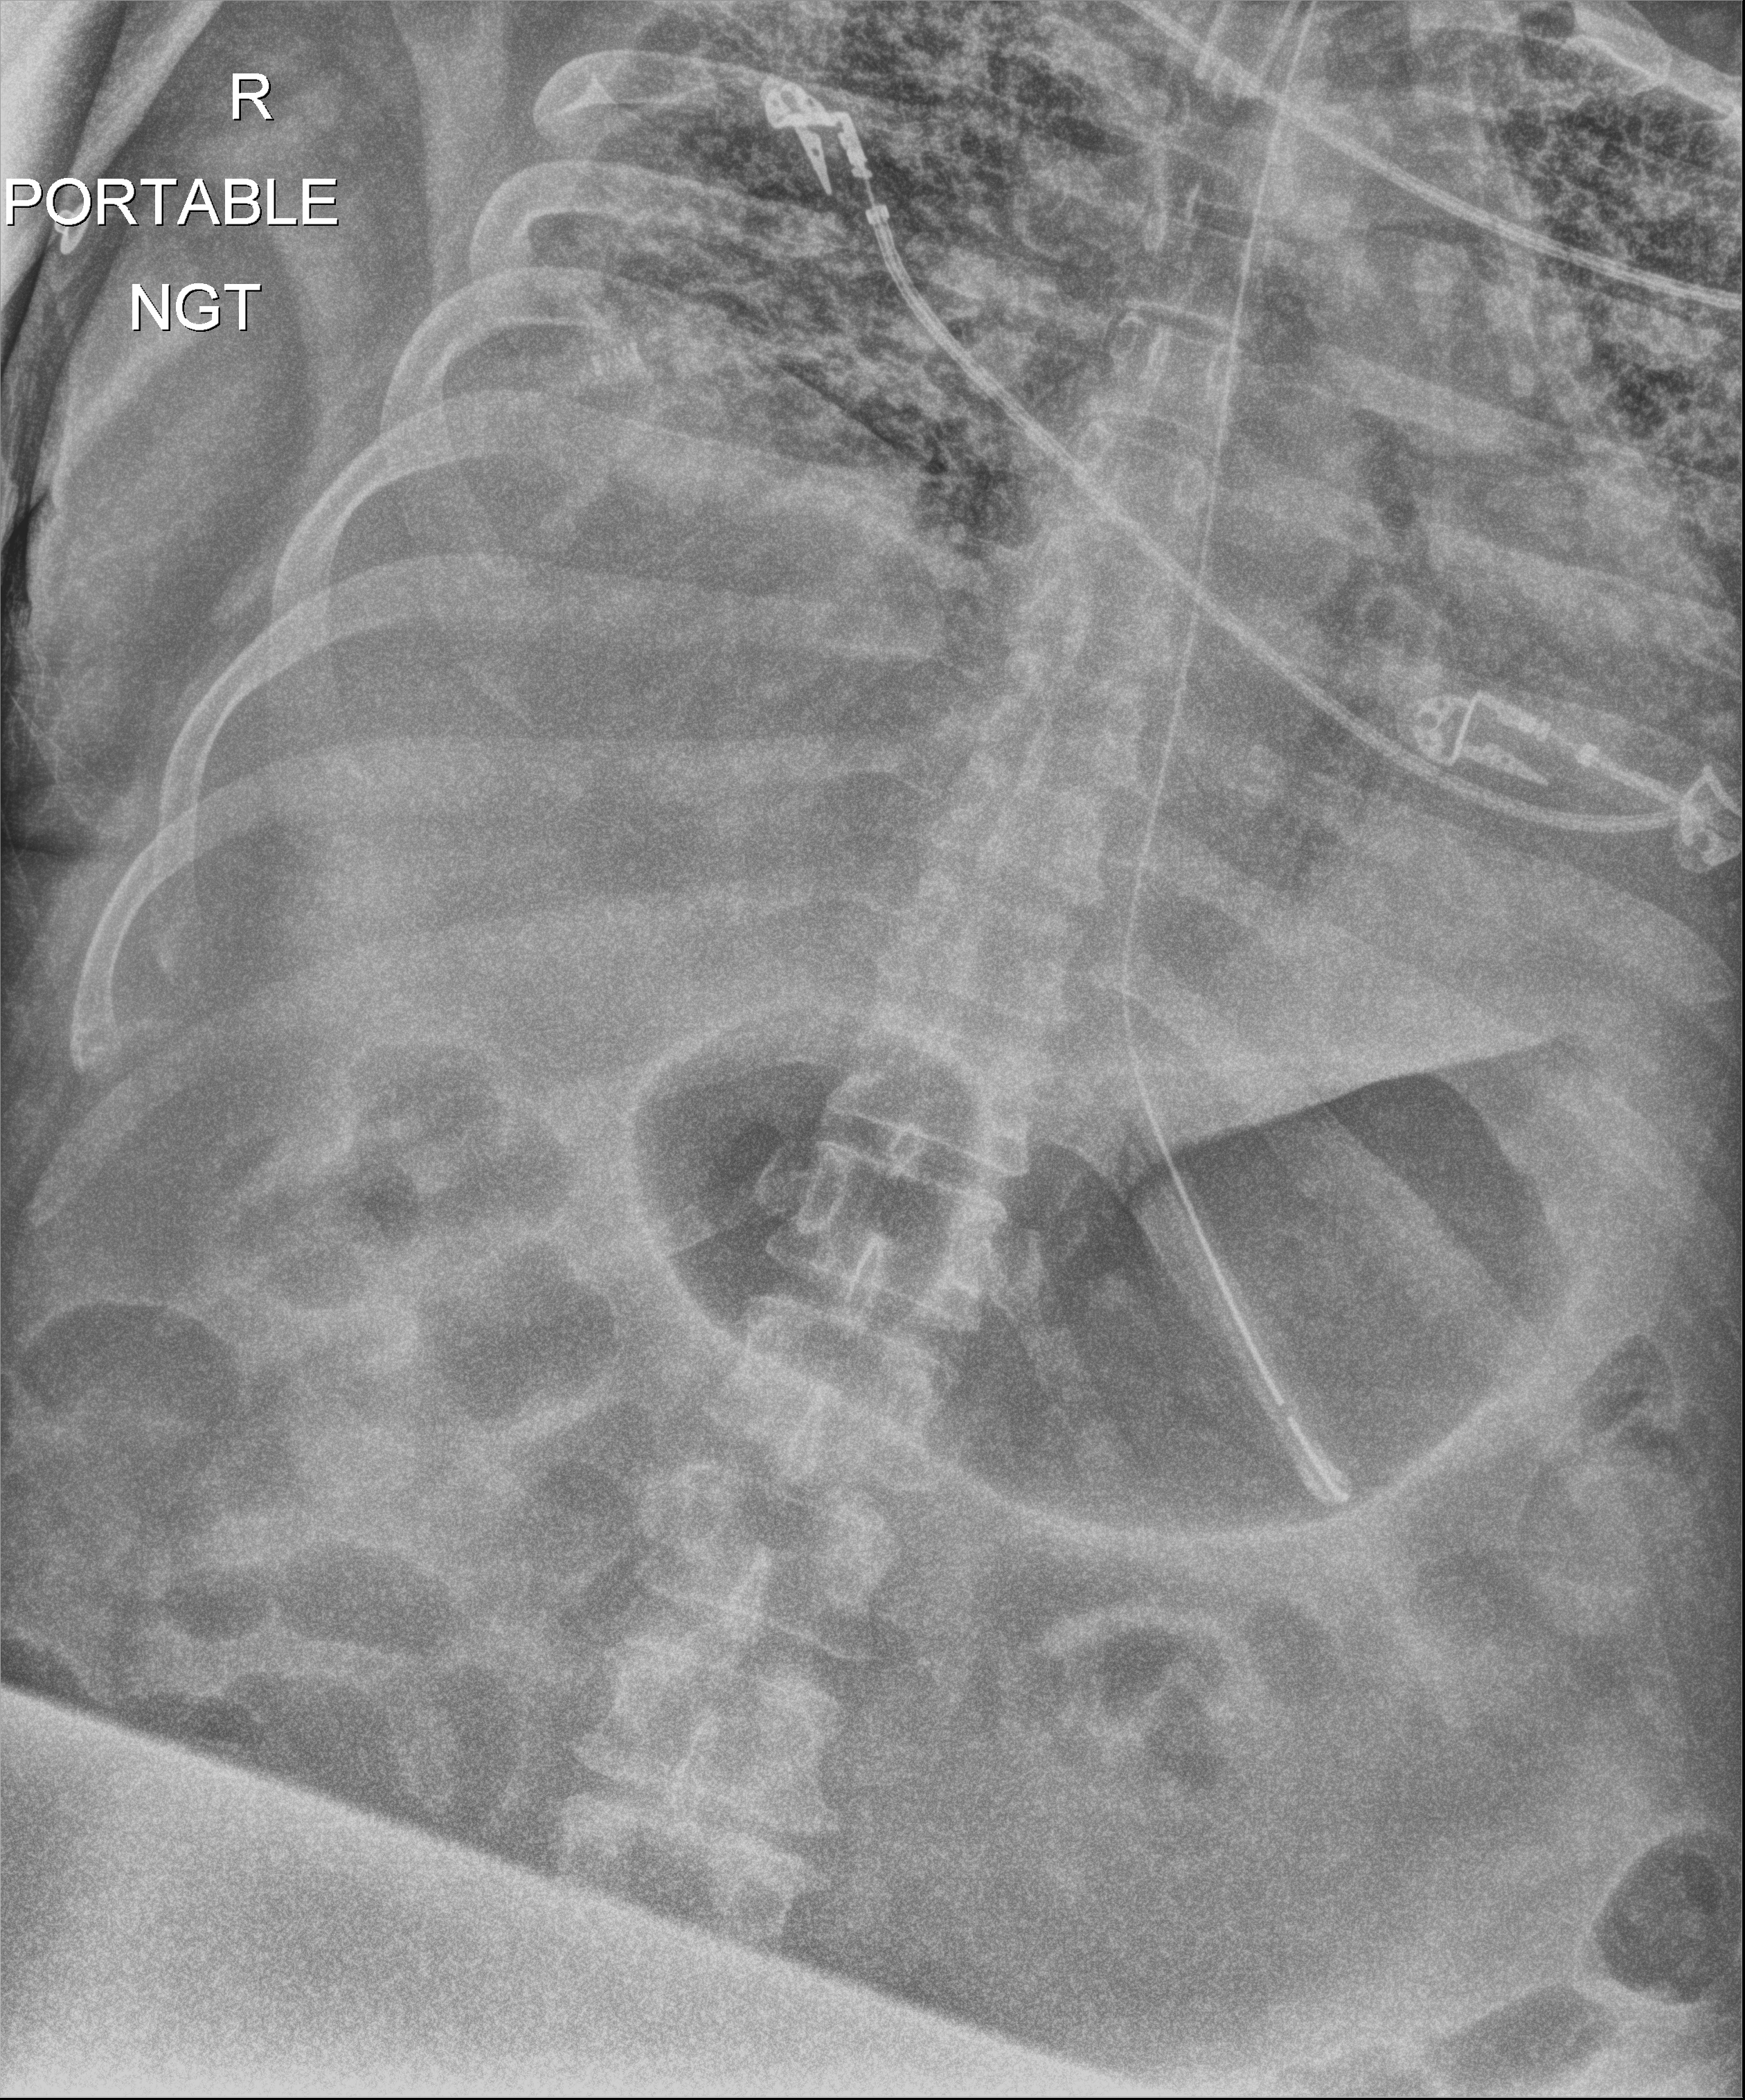
Chest X-ray (portable), anteroposterior (AP) projection. Patient hospitalised with COVID-19; male, aged 18–59 years.
Admission-level facts for this patient (not findings on this image; timing relative to this image not recorded):
- length of hospital stay: 96 days
- other chronic lung disease (admission record): no
- mechanically ventilated during this hospital stay: yes